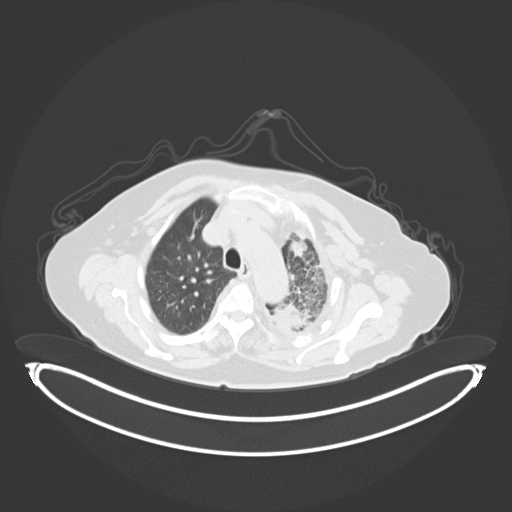
Chest CT, one axial slice; slice 221 of 284 in the series (ordered by position); reconstruction kernel B30f; lung window (W 1500 / L -600 HU); 3 mm slice thickness; 512 × 512 image matrix, field of view 500 × 500 mm. Patient: female, 75 years. Case-level facts recorded for this patient, not image findings: clinical TNM (as recorded): T3 N3 M1.
Annotated regions visible in this slice (bounding box drawn by a radiologist):
- lung tumour (recorded histology: adenocarcinoma): bounding box <266,297,315,335> (left, top, right, bottom; pixels)